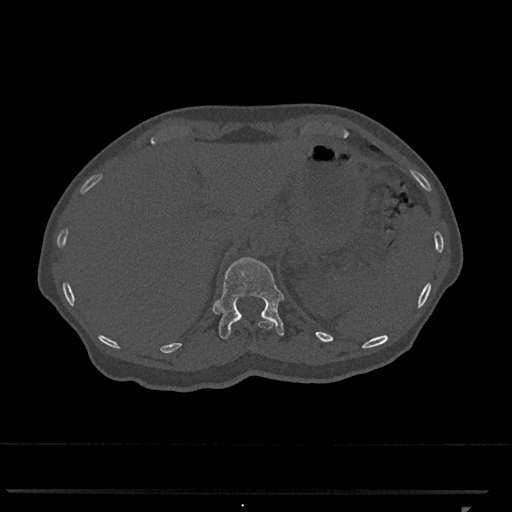
CT including the spine, one axial slice; slice 479 of 793 in the series (ordered by position); reconstruction kernel Br40s/3; 120 kVp; bone window (W 1800 / L 400 HU); 0.5 mm slice thickness; 512 × 512 image matrix, field of view 380 × 380 mm. Female patient, age 62 years. From the clinical record (not read from this slice): primary cancer: renal.
Structures marked on this image (semi-automatically segmented with operator editing):
- T11 vertebra: bounding box <245,320,274,330> (left, top, right, bottom; pixels)
- T12 vertebra: <214,257,284,339>